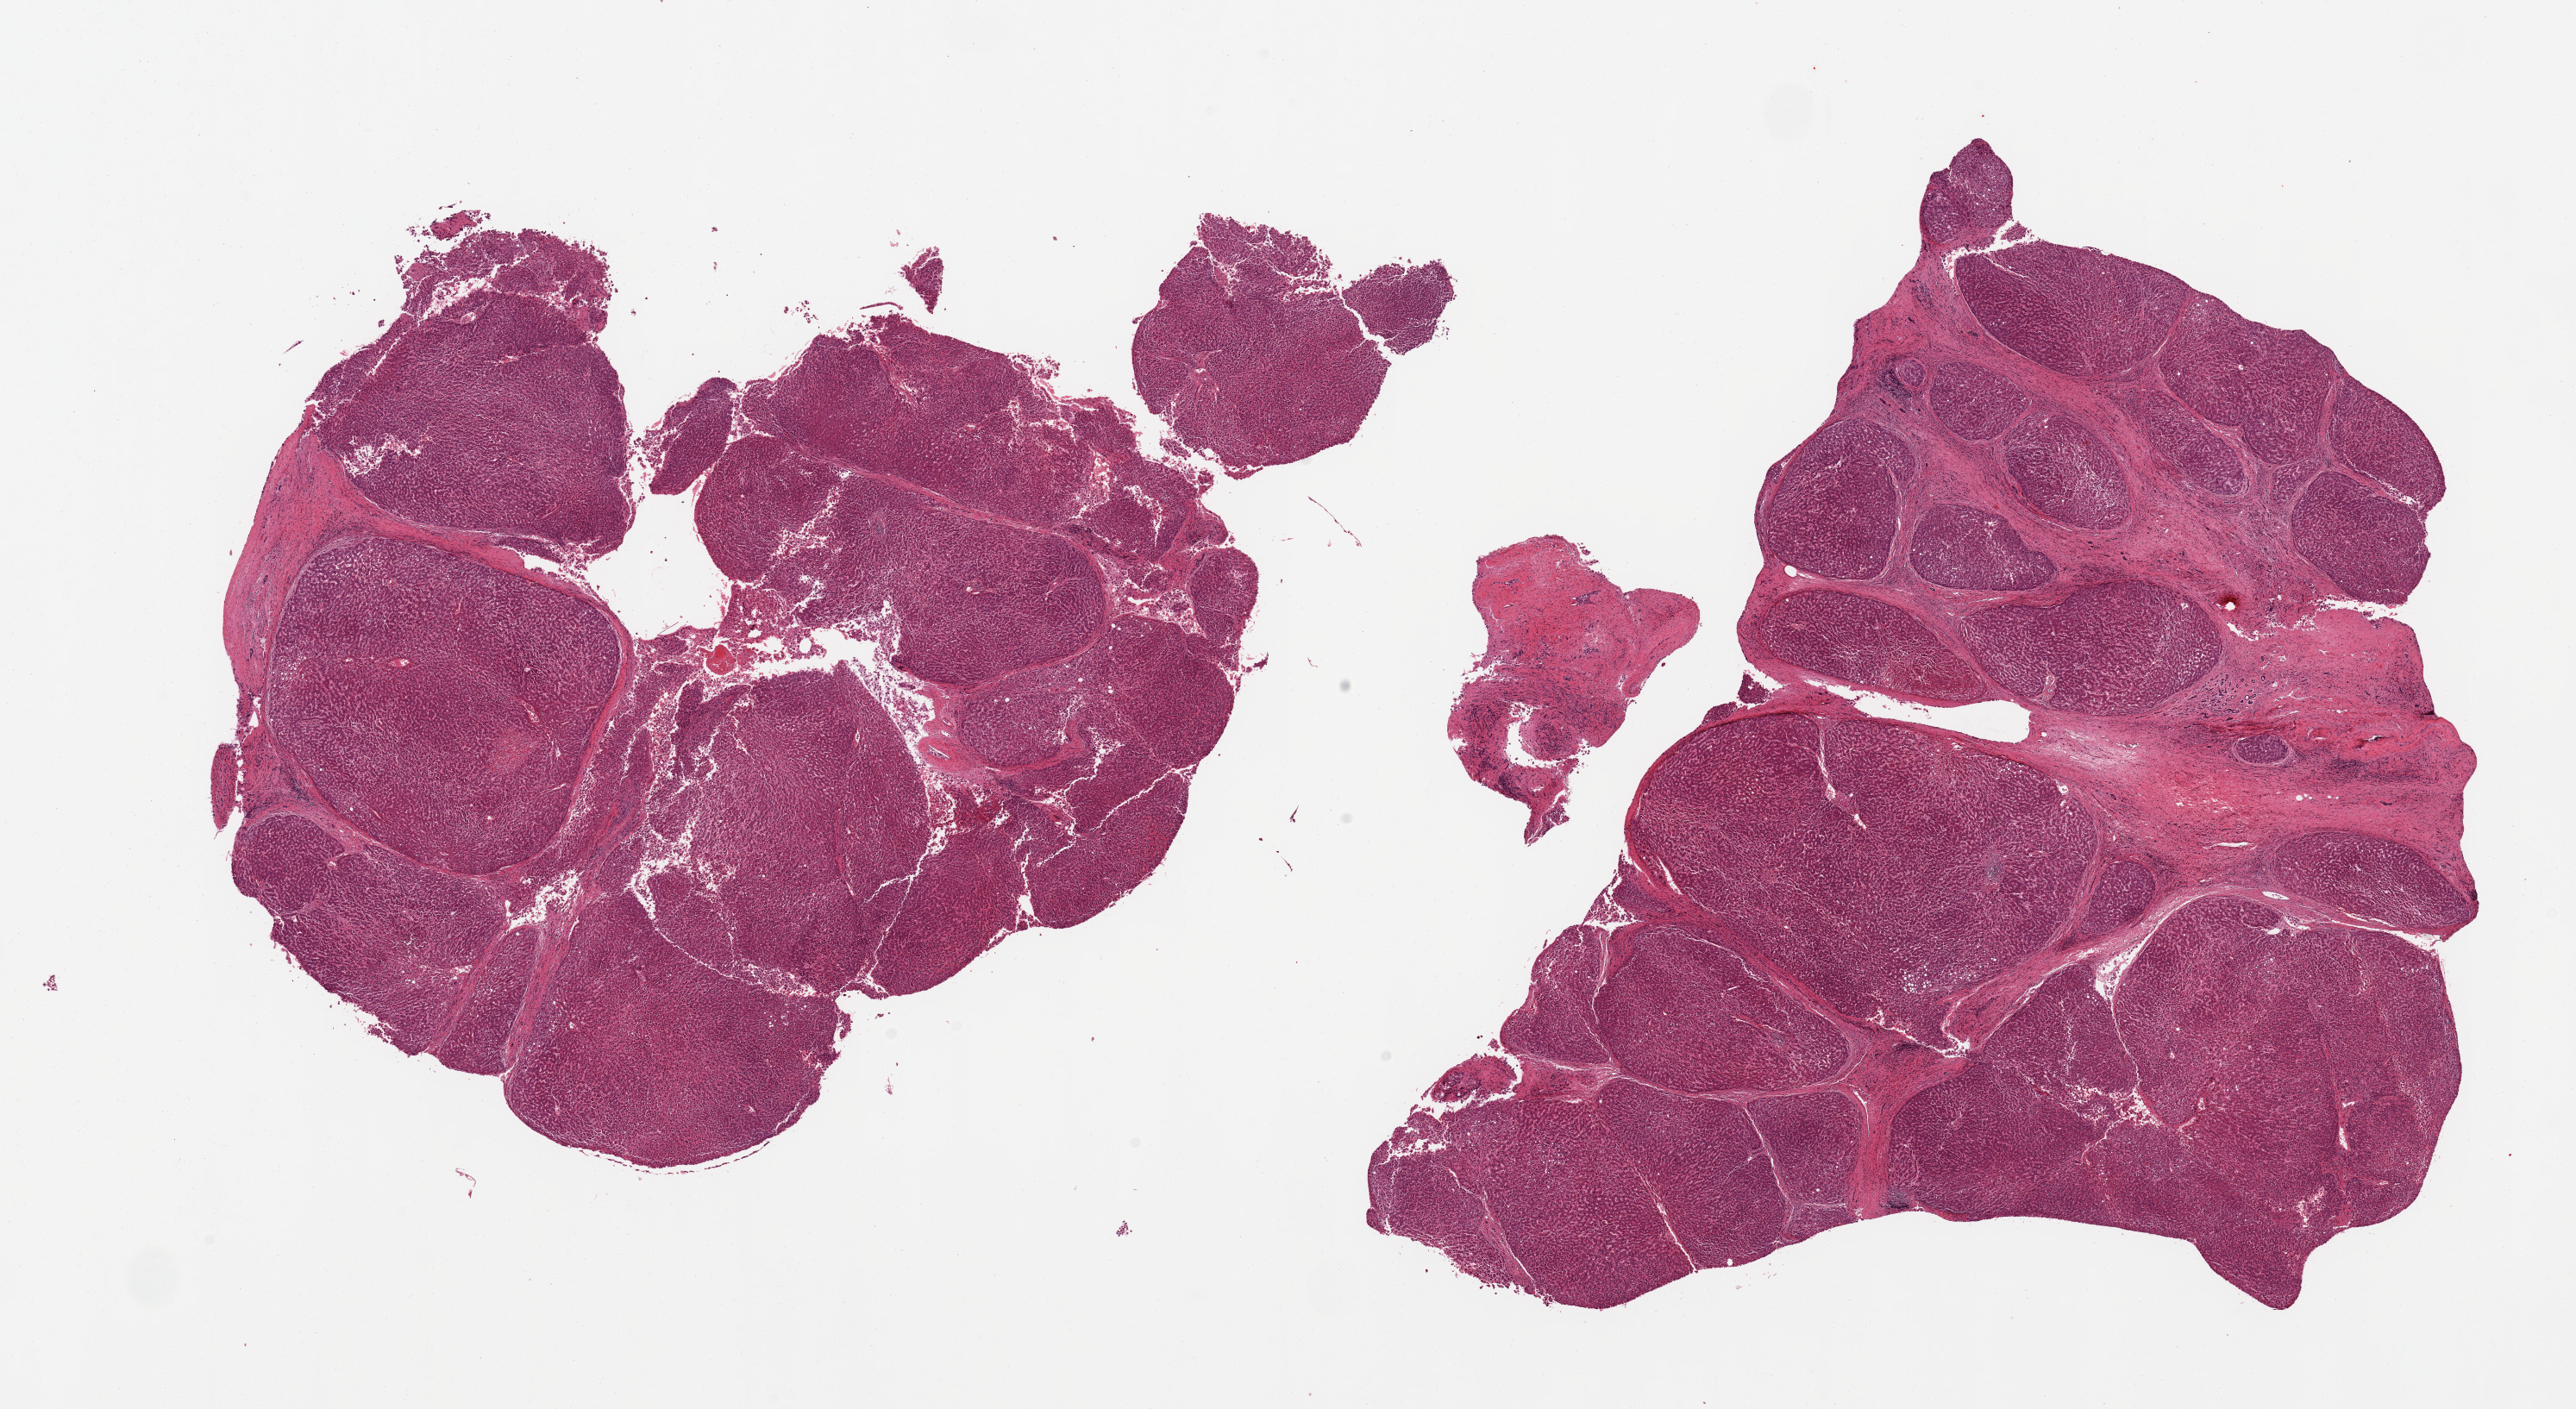
Haematoxylin and eosin whole-slide image, brightfield, whole scanned area (about 23.6 x 12.9 mm) shown as a low-resolution overview. PAXgene-fixed, paraffin-embedded tissue. Target tissue: liver. Donor tissue sample. Donor: male.
- reviewer comment on this tissue sample: 2 pieces; cirrhosis